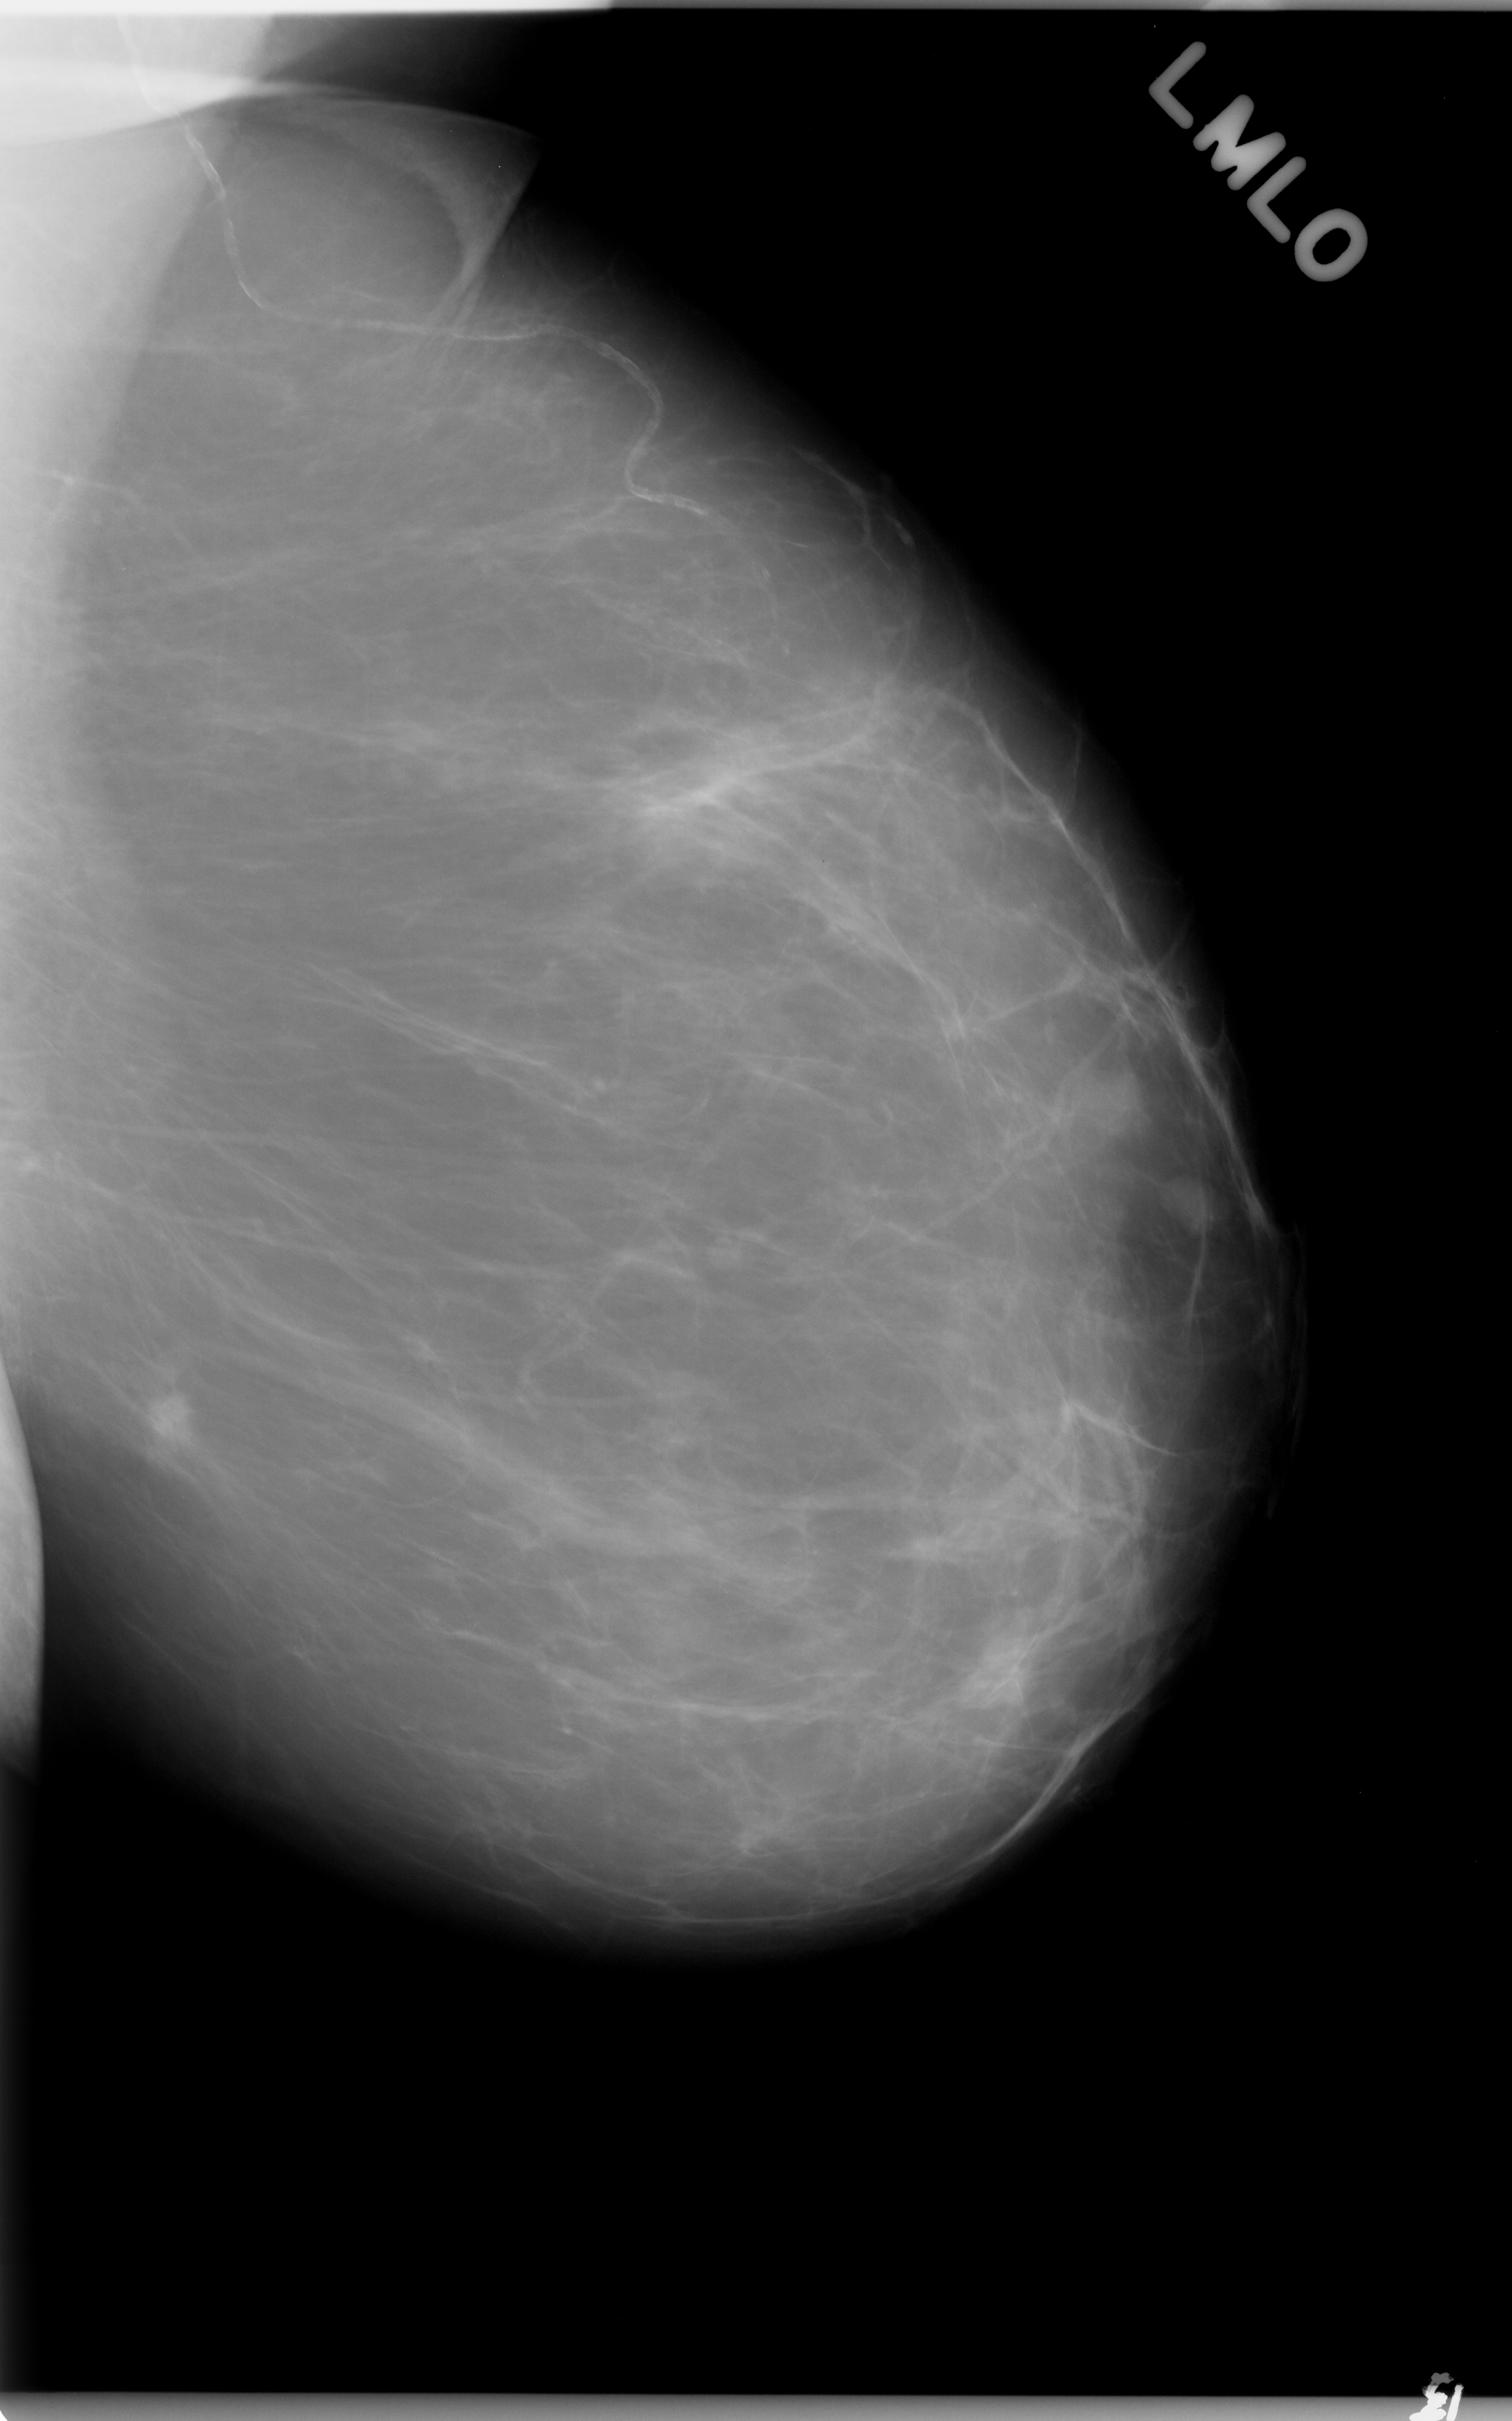
Scanned film-screen mammogram; left breast; MLO view; breast composition: almost entirely fatty (BI-RADS density category 1 of 4).
Mass, shape irregular, margins spiculated; BI-RADS assessment category 5; pathology (as recorded): malignant.